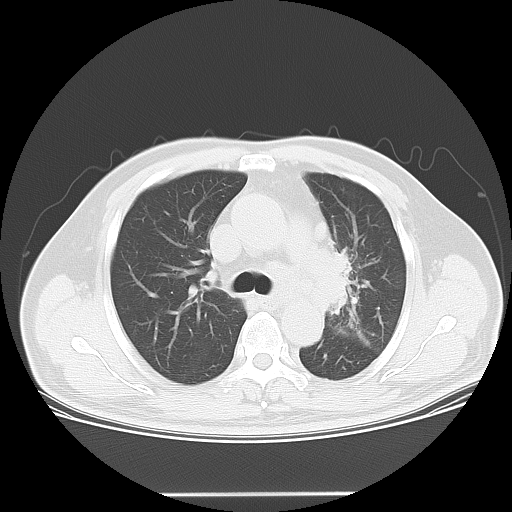
Chest CT, one axial slice. Slice 38 of 55 in the series (ordered by position). Reconstruction kernel LUNG. Lung window (W 1500 / L -600 HU). 5 mm slice thickness. 512 × 512 image matrix, field of view 398 × 398 mm. Male patient, age 61 years. From the clinical record (not read from this slice): clinical TNM (as recorded): T3 N1 M1; histopathological grade: G3.
Structures marked on this image (rectangle marked by the reading radiologist):
- lung tumour (recorded histology: small cell carcinoma): bounding box [x1, y1, x2, y2] px = [316, 234, 359, 328]